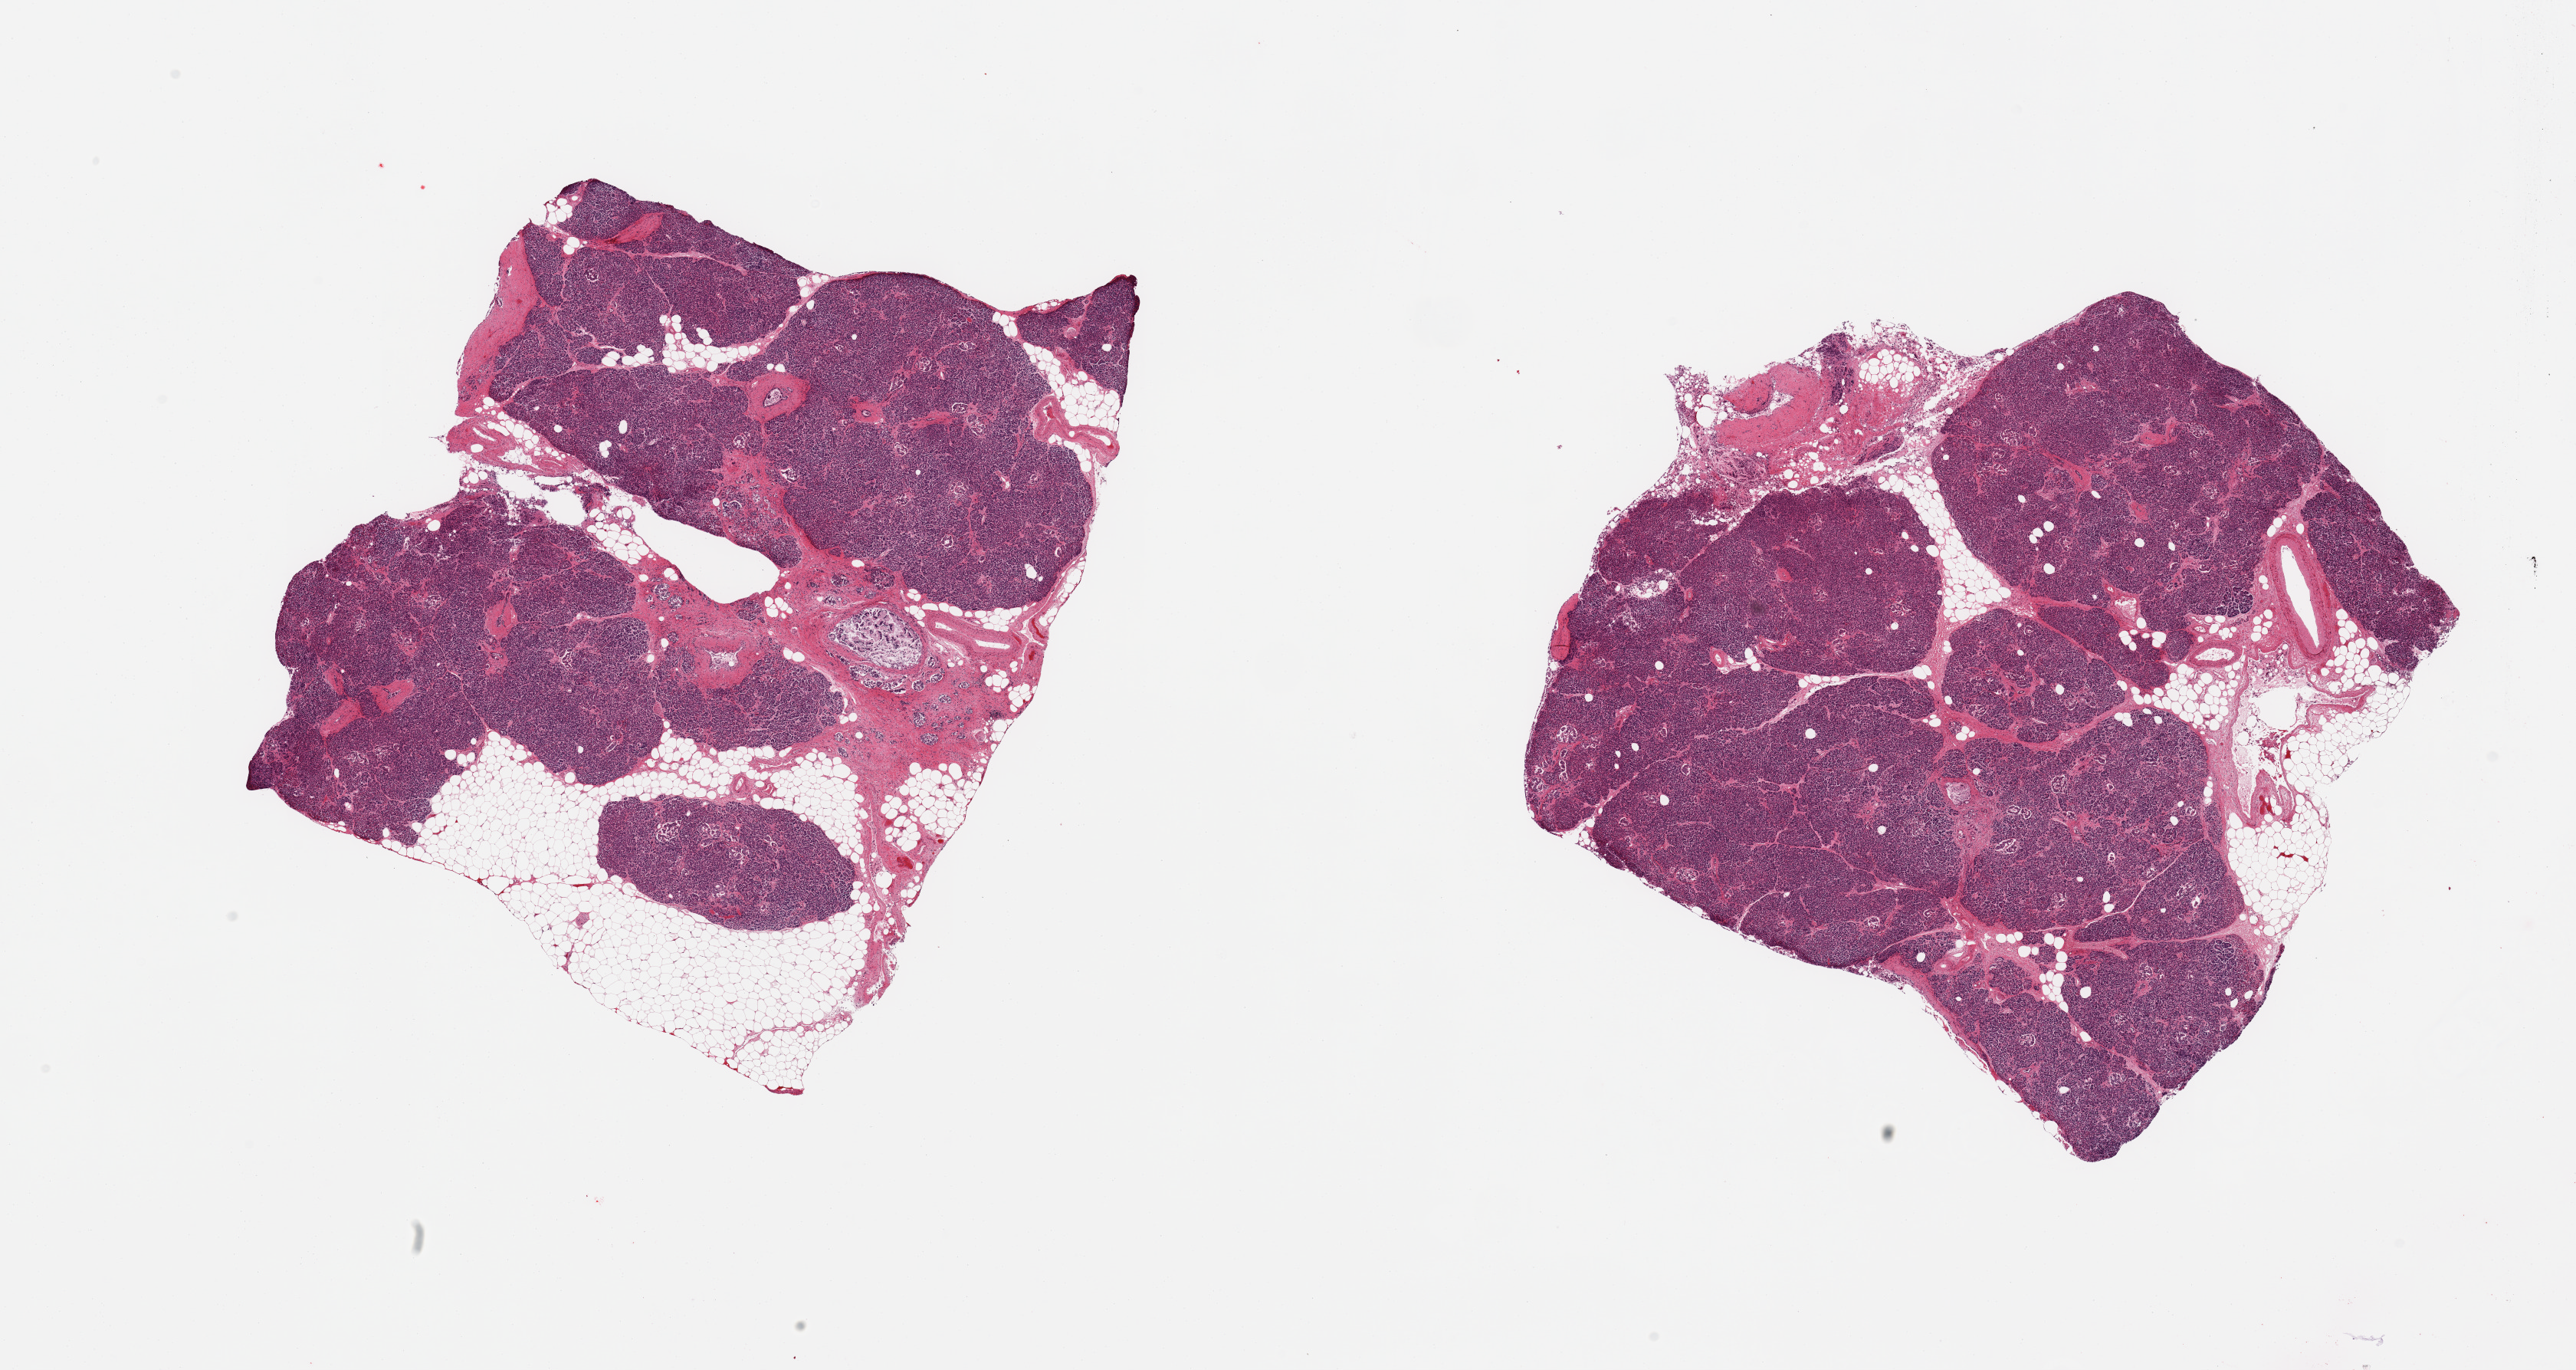
Haematoxylin and eosin whole-slide image, brightfield, whole scanned area (about 26.6 x 14.1 mm, slide scanned at 20x) shown as a low-resolution overview; PAXgene-fixed, paraffin-embedded tissue; section of pancreas (target tissue); donor tissue sample. Donor: male.
Pathologist's review note for this sample: 2 pieces; 10 to 20% internal fat; desquamated ductal epithelium; islets well visualized.